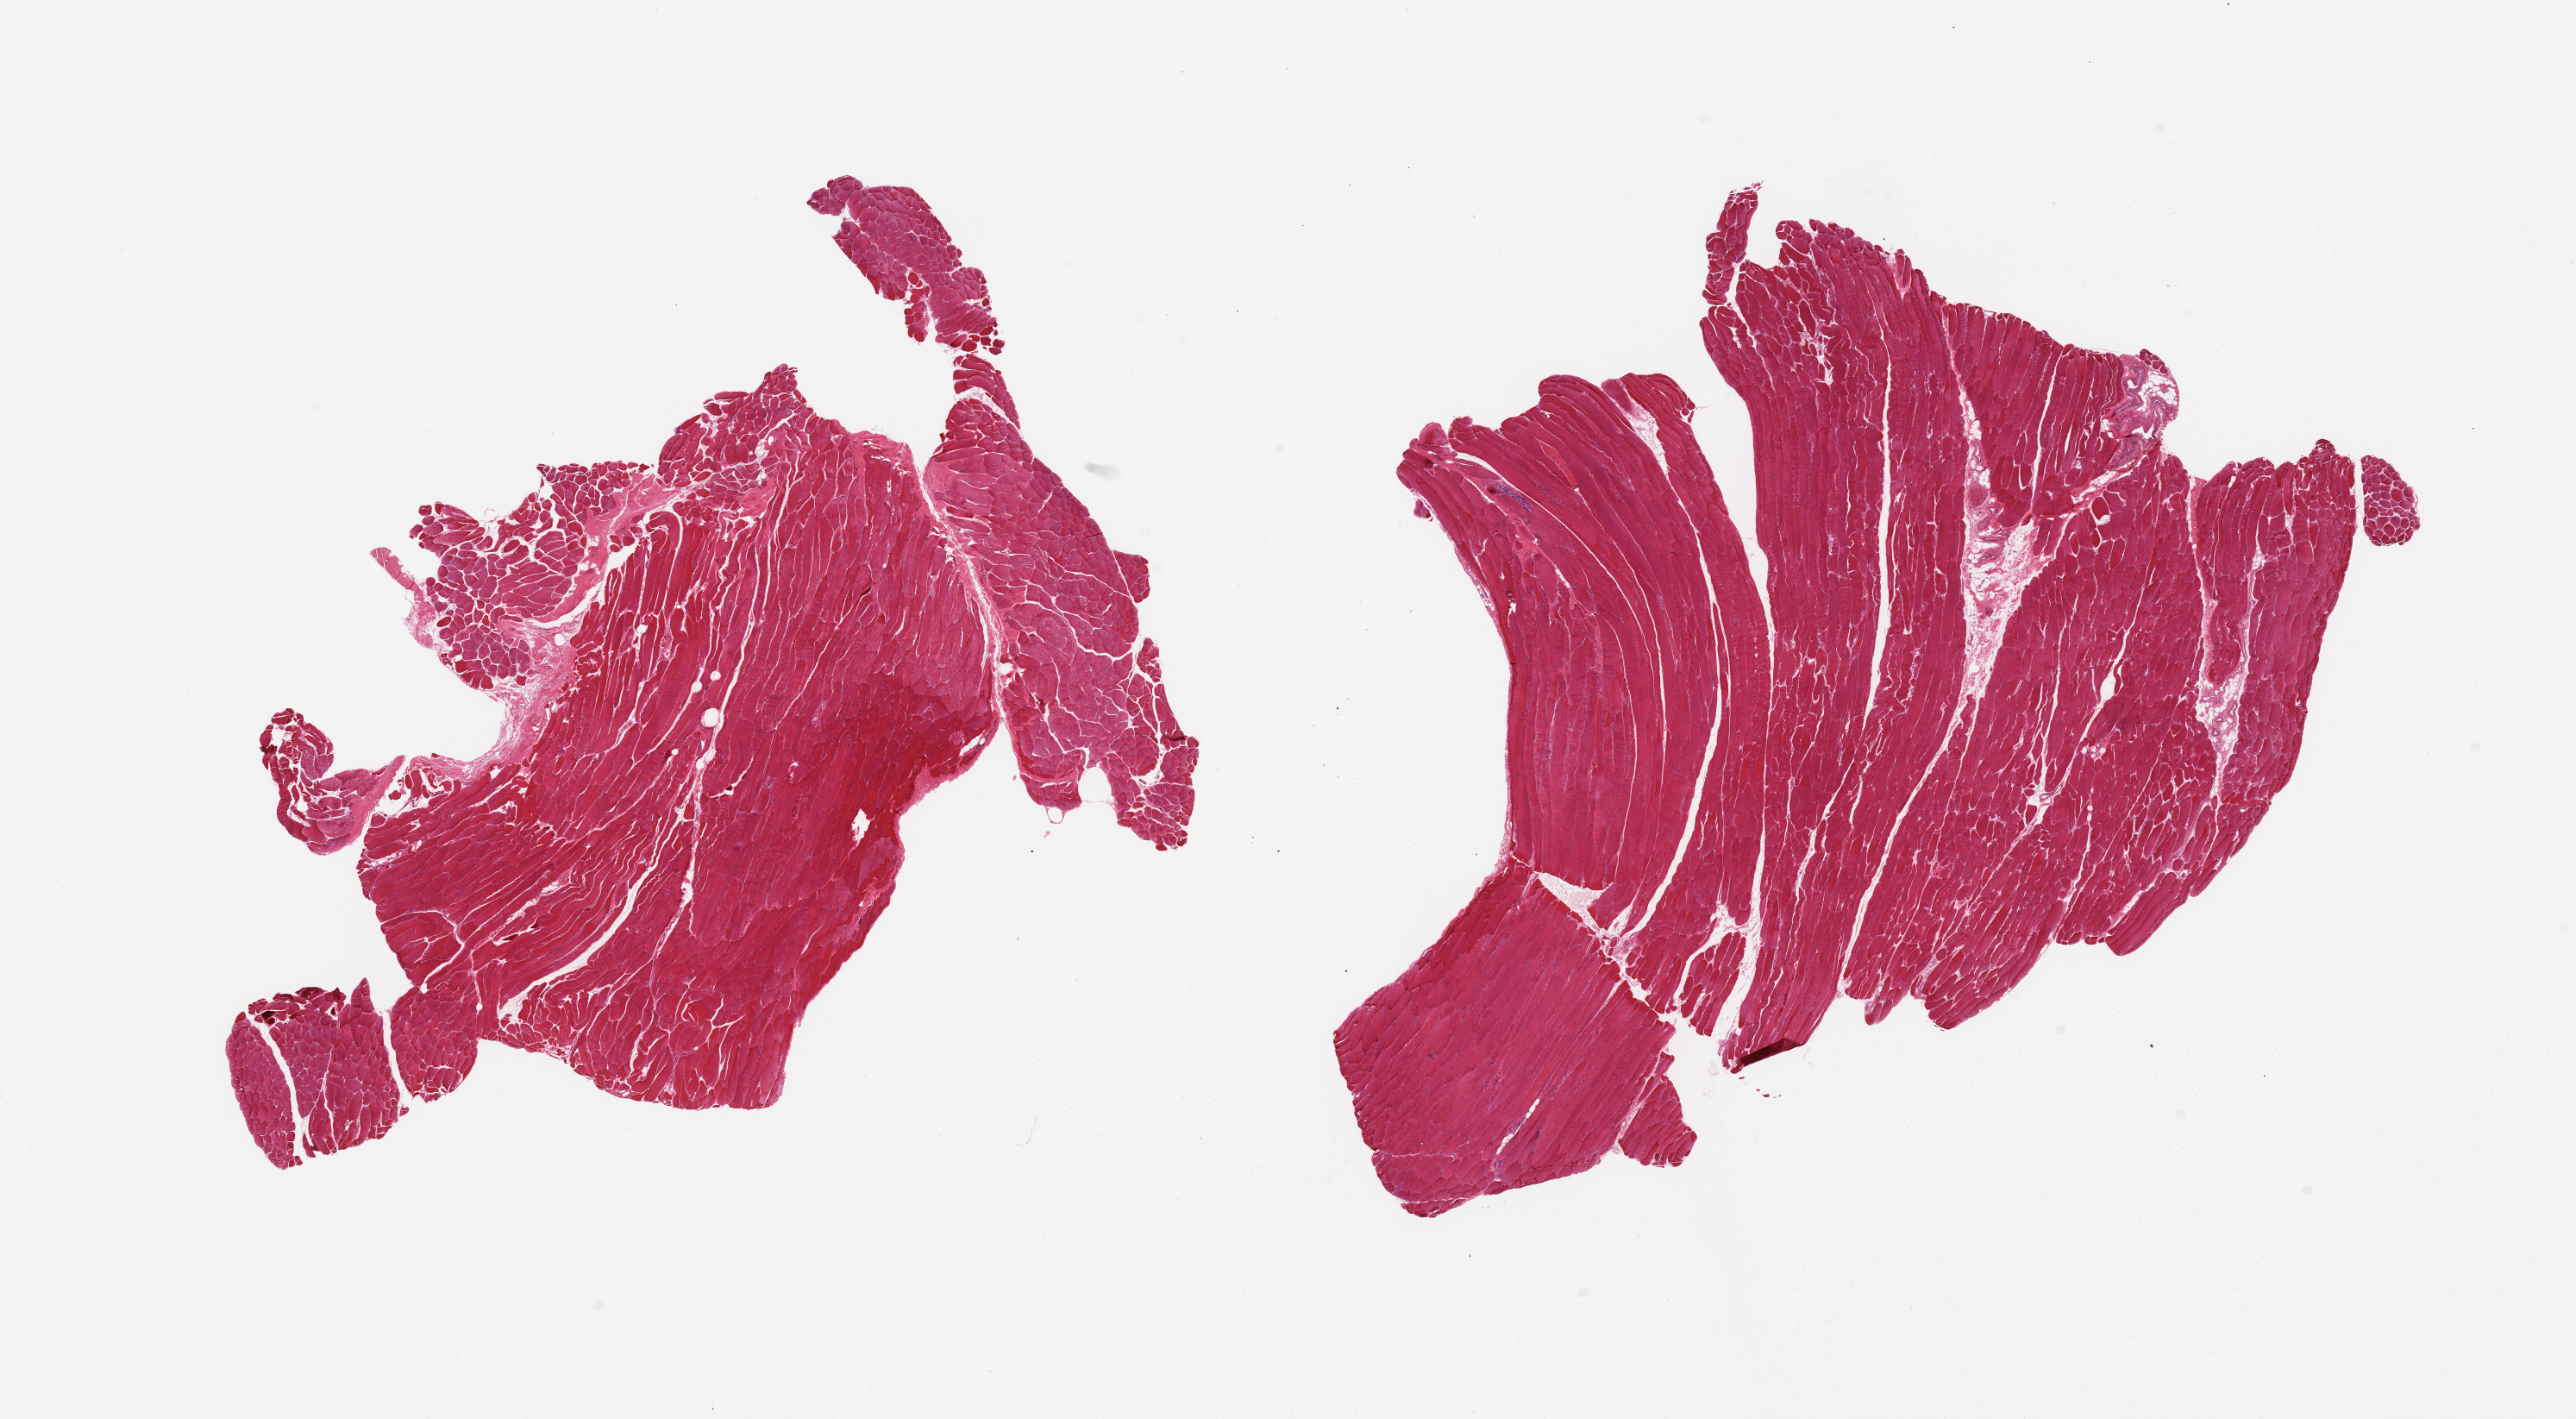
H&E whole-slide image, whole scanned area (about 23.6 x 13.0 mm, from a 20x scan) shown as a low-resolution overview. PAXgene-fixed, paraffin-embedded tissue. Target tissue: skeletal muscle. Tissue donor sample. Donor: male.
- review note (as recorded): 2 pieces; target skeletal muscle fibers